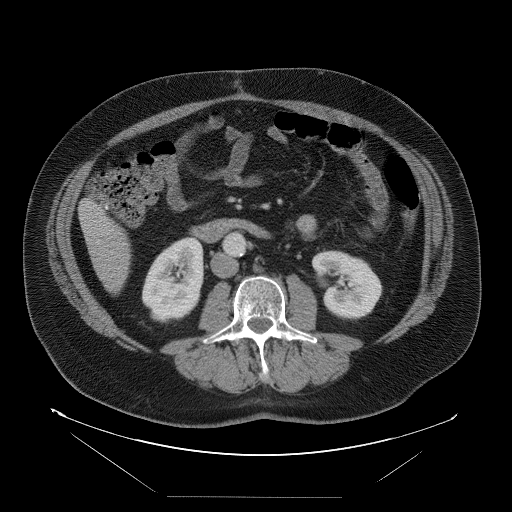
Contrast-enhanced abdominal CT, one axial slice; slice 21 of 114 in the series (ordered by position); 120 kVp; soft-tissue window (W 400 / L 40 HU); 5 mm slice thickness; 512 × 512 image matrix, field of view 500 × 500 mm. Male patient, age 61 years. From the clinical record (not read from this slice): diagnosis: colorectal cancer liver metastases, imaged before liver resection; multiple liver metastases: no; largest metastasis: 6.5 cm; chemotherapy before resection: no.
Structures marked on this image (outlined manually by an expert reader):
- liver: box from (x=81, y=201) to (x=131, y=294) px